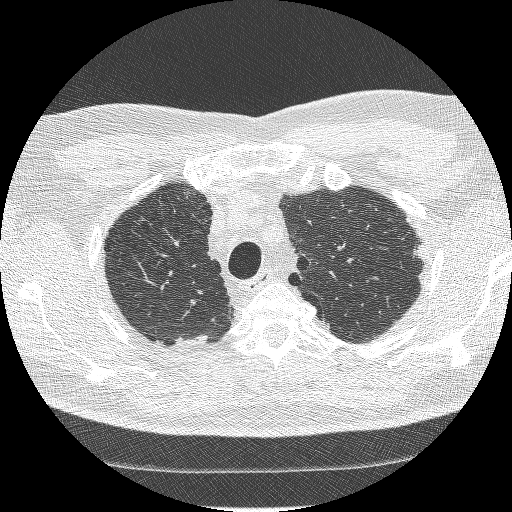
Chest CT (low-dose screening protocol), one axial image. First (baseline) screen. Lung window (W 1500 / L -600 HU). 1.25 mm slice thickness. Lung (sharp) reconstruction kernel (BONE). Male, age 66 years at enrolment.
Expert-annotated lung lesion, bounding box <398,232,435,268> (left, top, right, bottom; pixels). The exam's reader record, not a measurement of the box and not confirmed to be the same lesion: non-calcified nodule or mass ≥4 mm, right lower lobe, 45 × 19 mm, spiculated (stellate) margins, soft tissue attenuation. Note: the box lies in the patient's left hemithorax on this image, whereas the reader's record names the right lung; they may be different findings. Official screen result: positive, change unspecified: nodule(s) >= 4 mm or enlarging nodule(s), mass(es), or other non-specific abnormalities suspicious for lung cancer. Later outcome: lung cancer diagnosed 960 days after this screen — adenocarcinoma, NOS, left upper lobe, poorly differentiated (G3), stage IB (AJCC 6th edition), 16 mm at pathology.